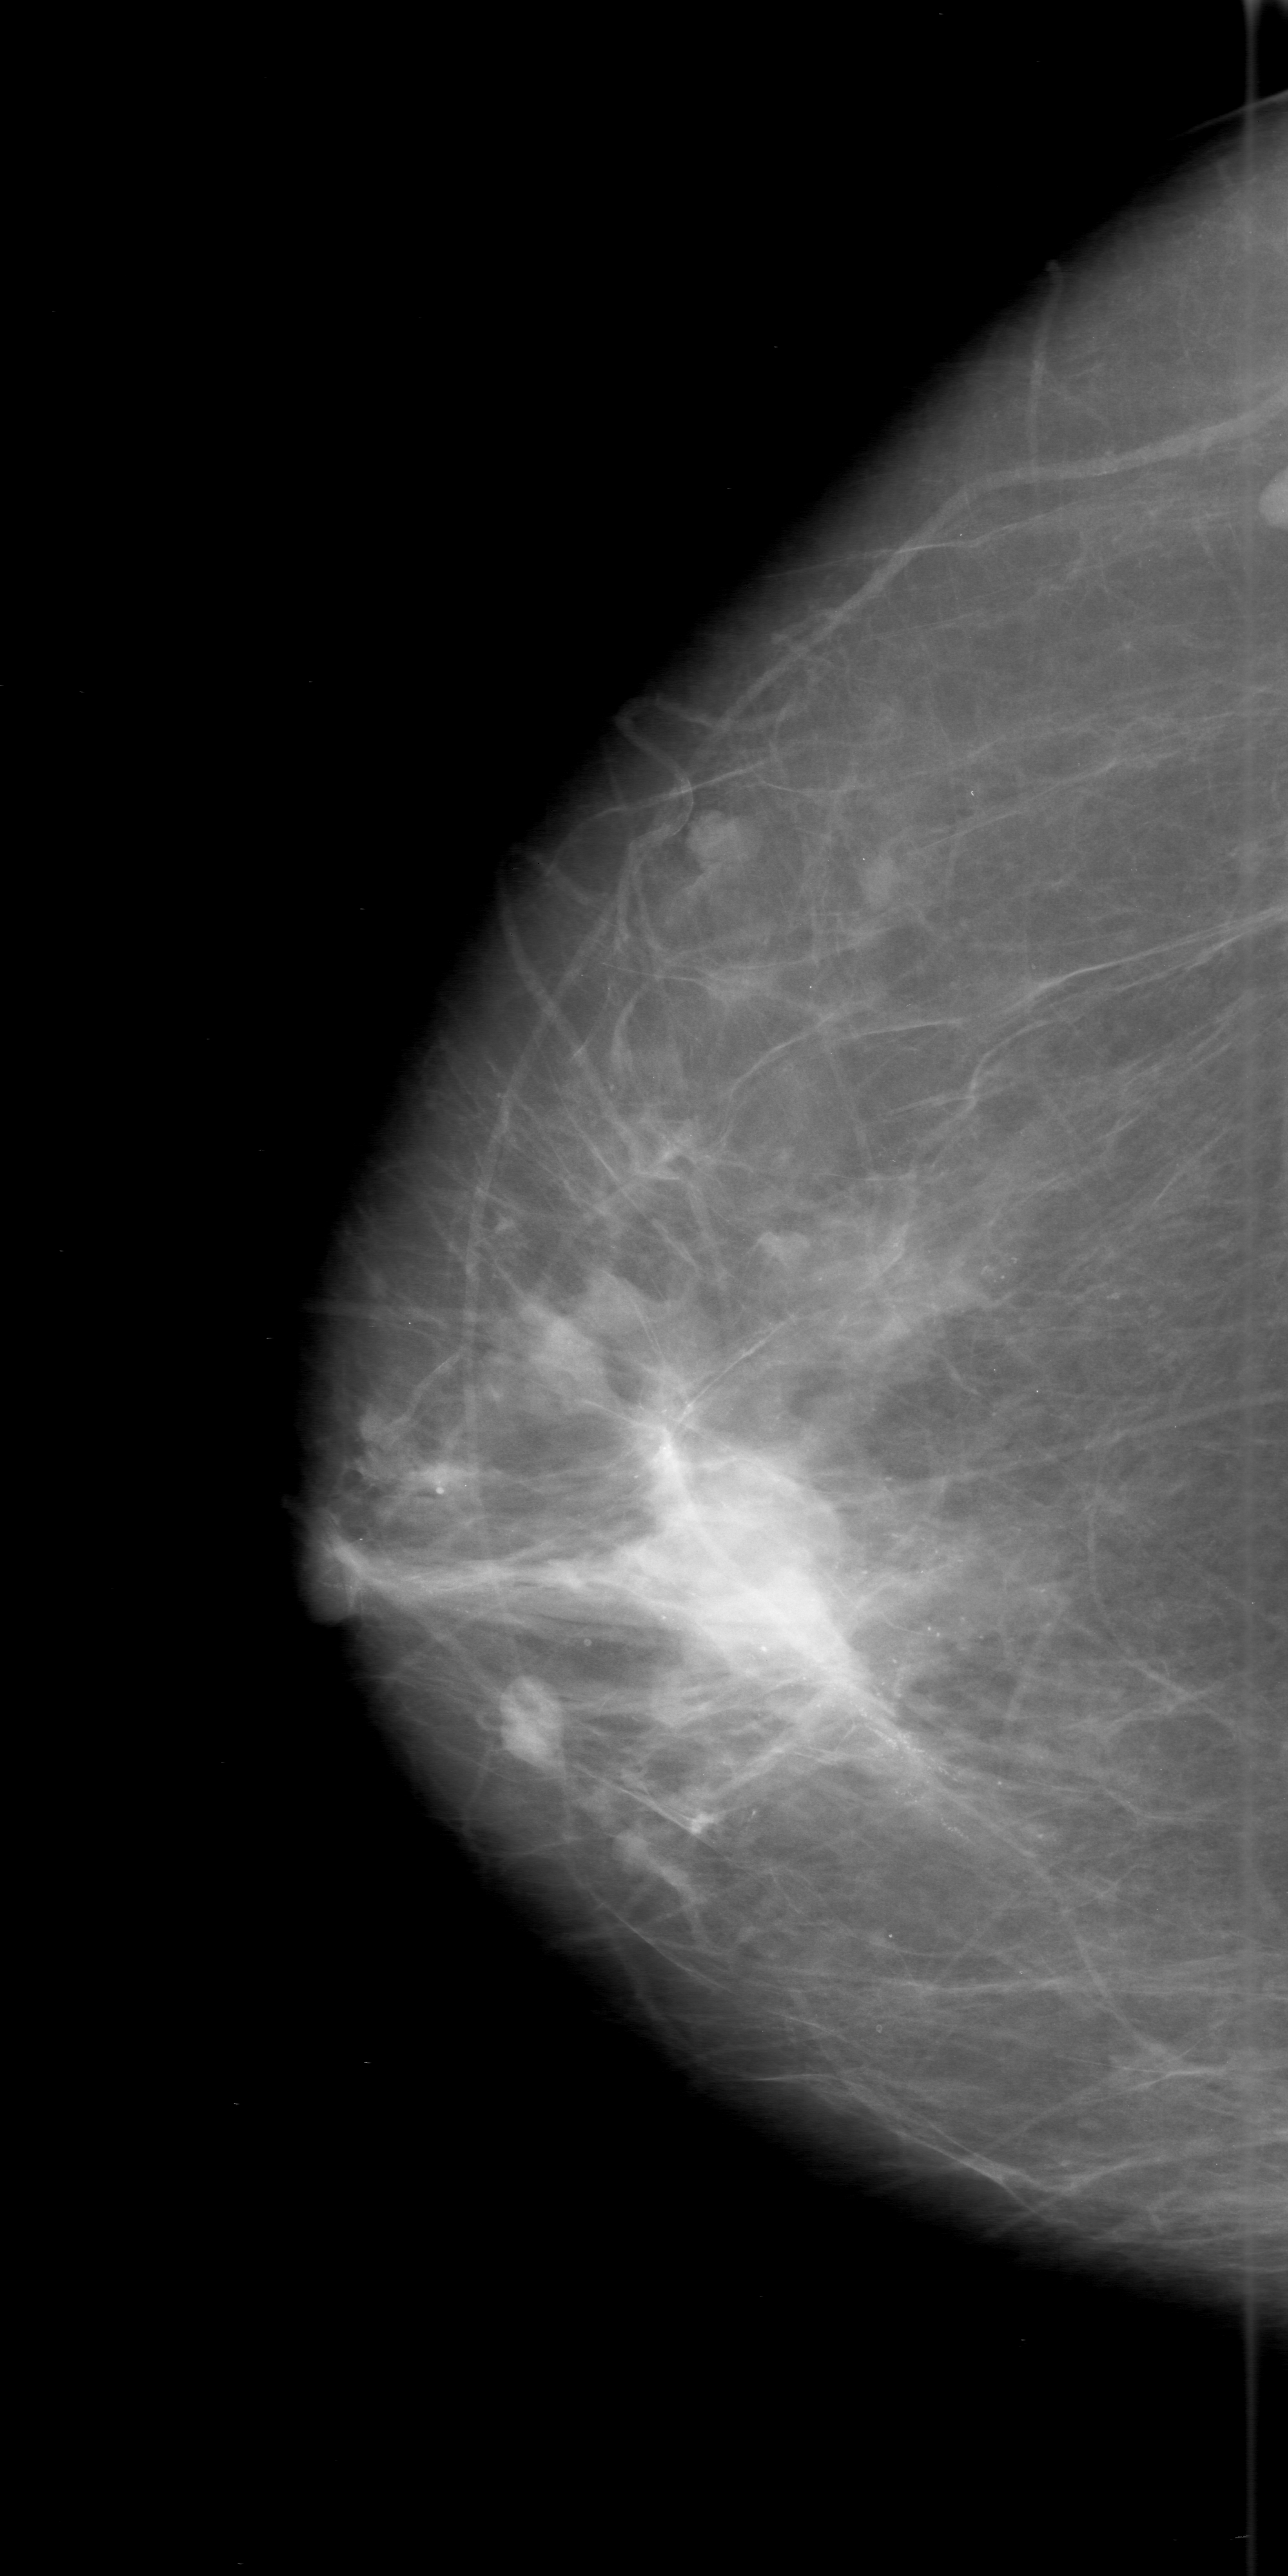
Mammogram (digitized film); right breast; craniocaudal (CC) view; BI-RADS breast density category 2 (scale 1–4); 1288 × 2576 image matrix.
Expert-marked regions of interest on this image (one box per marked abnormality):
- calcifications, morphology amorphous / pleomorphic, distribution segmental; BI-RADS assessment category 5; pathology result (as recorded, not read from the image): malignant: box from (x=372, y=1181) to (x=1236, y=1849) px